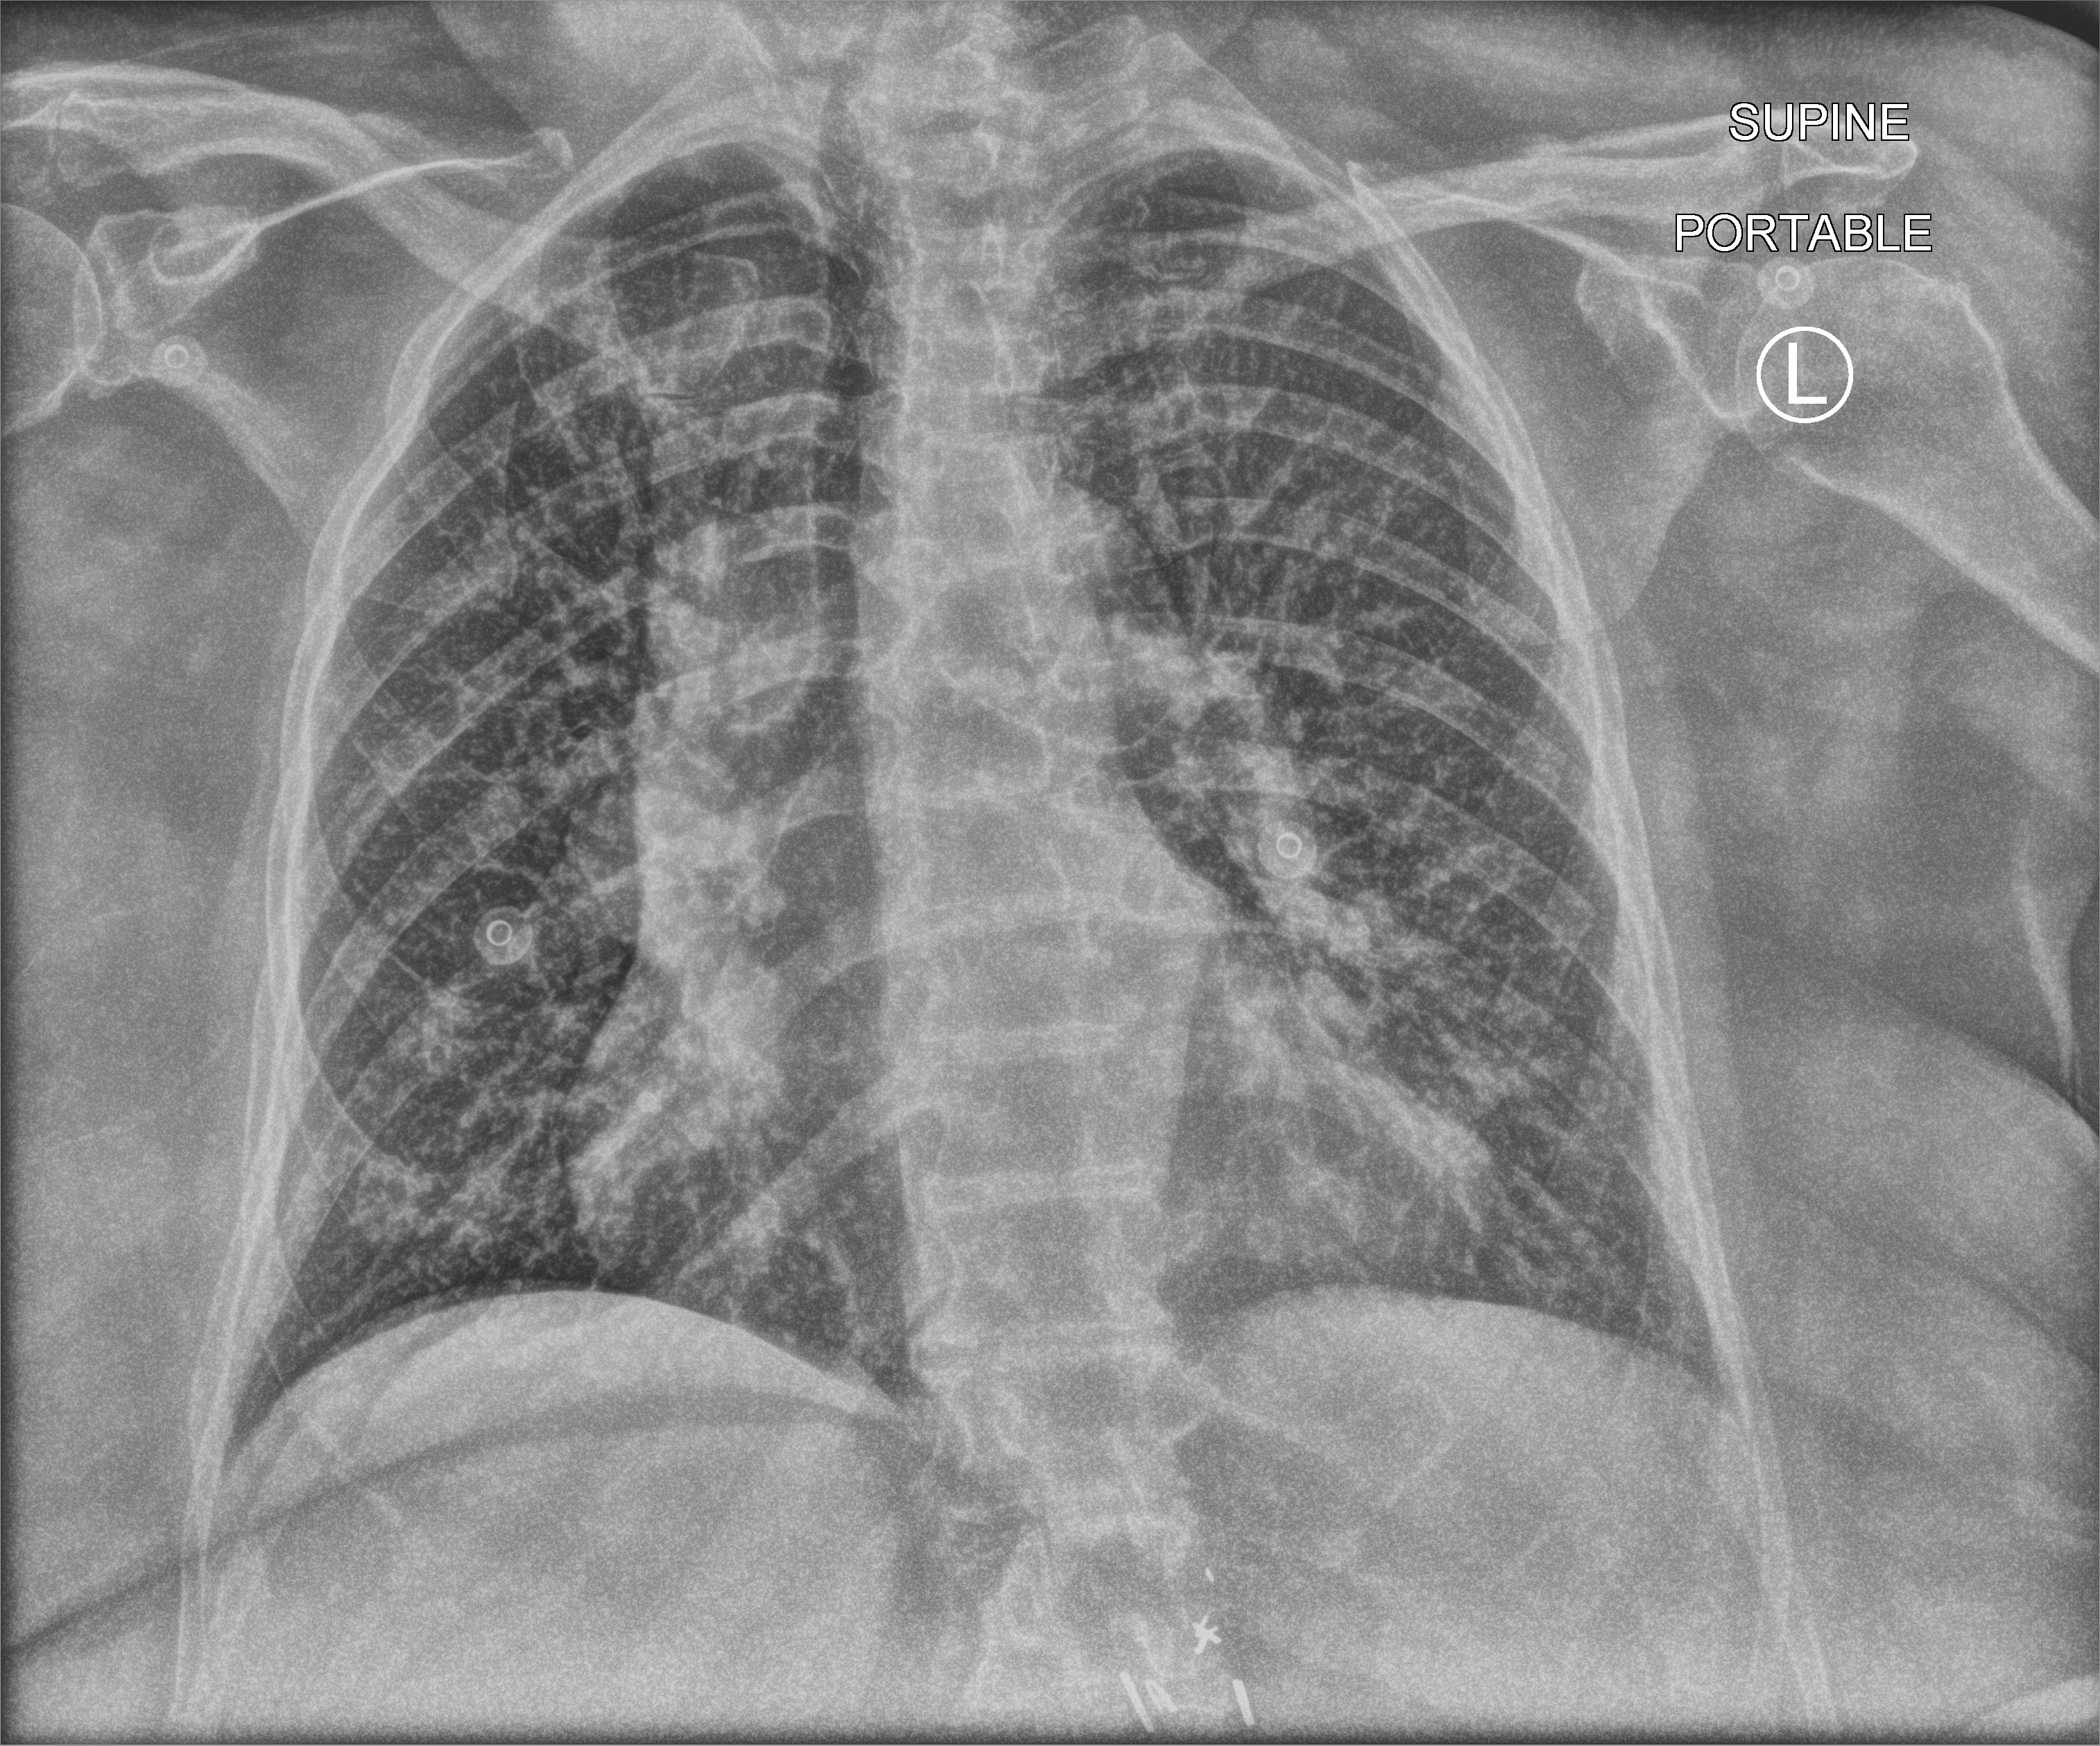
Bedside chest radiograph (computed radiography), anteroposterior (AP) projection. Patient hospitalised with COVID-19; female, aged 75–90 years.
Hospital-stay facts (about this admission, not read from this image; timing relative to this image not recorded): mechanically ventilated during this hospital stay: no.